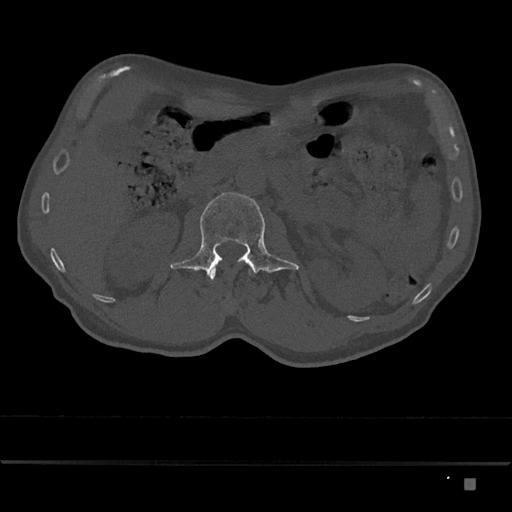
CT including the spine, one axial slice; position 489 of 797 along the scan axis; reconstruction kernel Br40s/3; bone window (W 1800 / L 400 HU); 512 × 512 image matrix, field of view 390 × 390 mm. Male patient, age 72 years. Case-level facts recorded for this patient, not image findings: primary cancer: prostate.
Annotated regions visible in this slice (semi-automatically segmented with operator editing):
- L1 vertebra: box from (x=210, y=268) to (x=251, y=280) px
- L2 vertebra: (x=170, y=192)–(x=299, y=277)